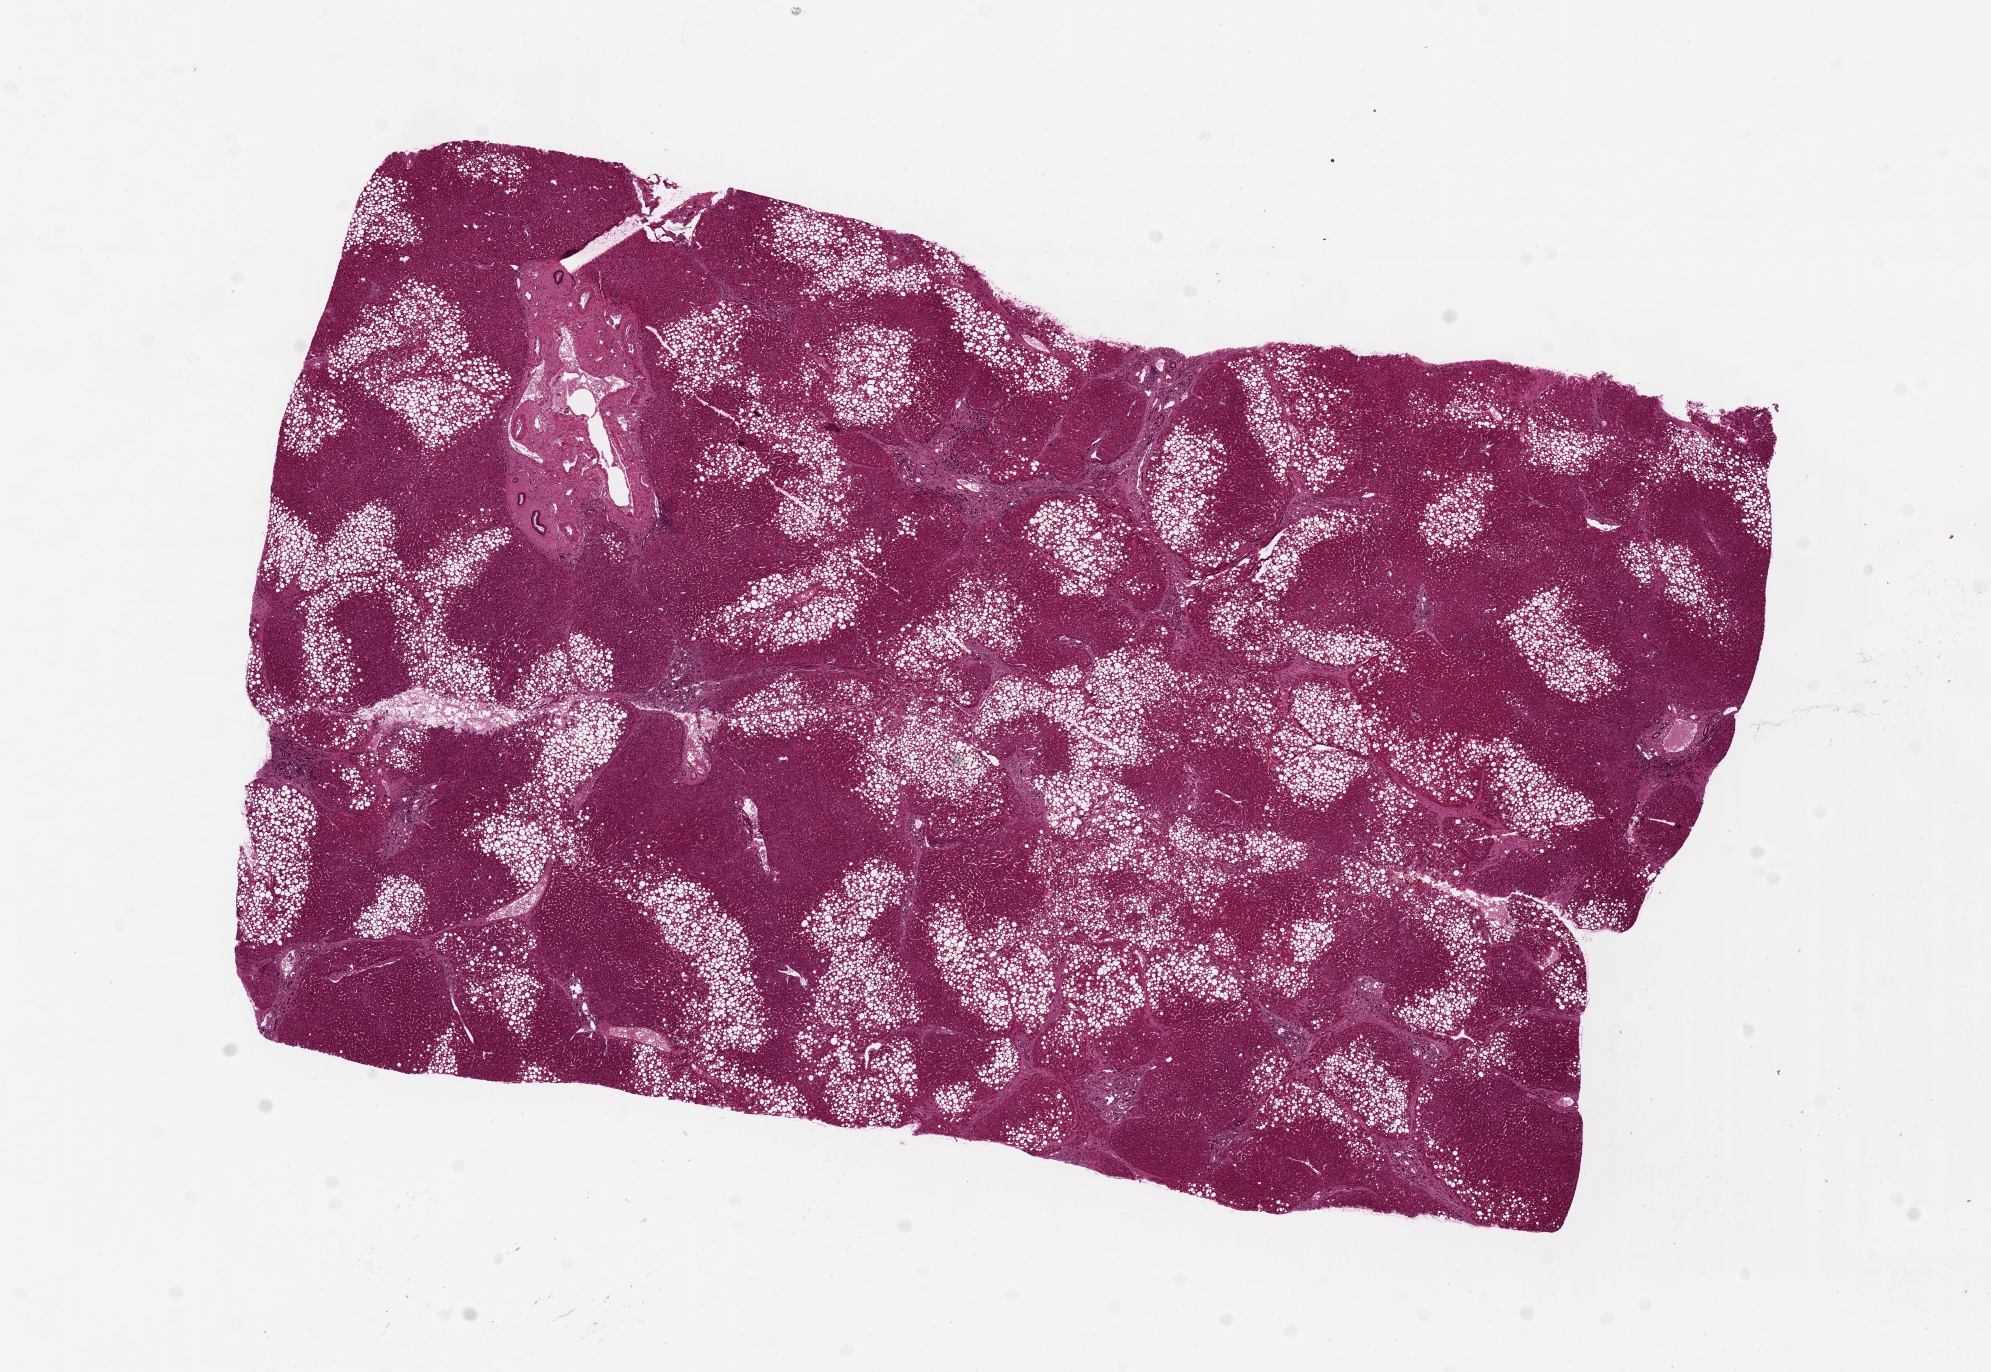
Digitized H&E-stained section — shown as a low-resolution overview of the whole scanned area (about 15.8 x 10.9 mm), PAXgene-fixed, paraffin-embedded tissue, section of liver (target tissue), tissue donor sample.
- review note (as recorded): Macovesicular steatosis (50%). Mild chronic hepatitis with severe bridging fibrosis/early cirrhosis